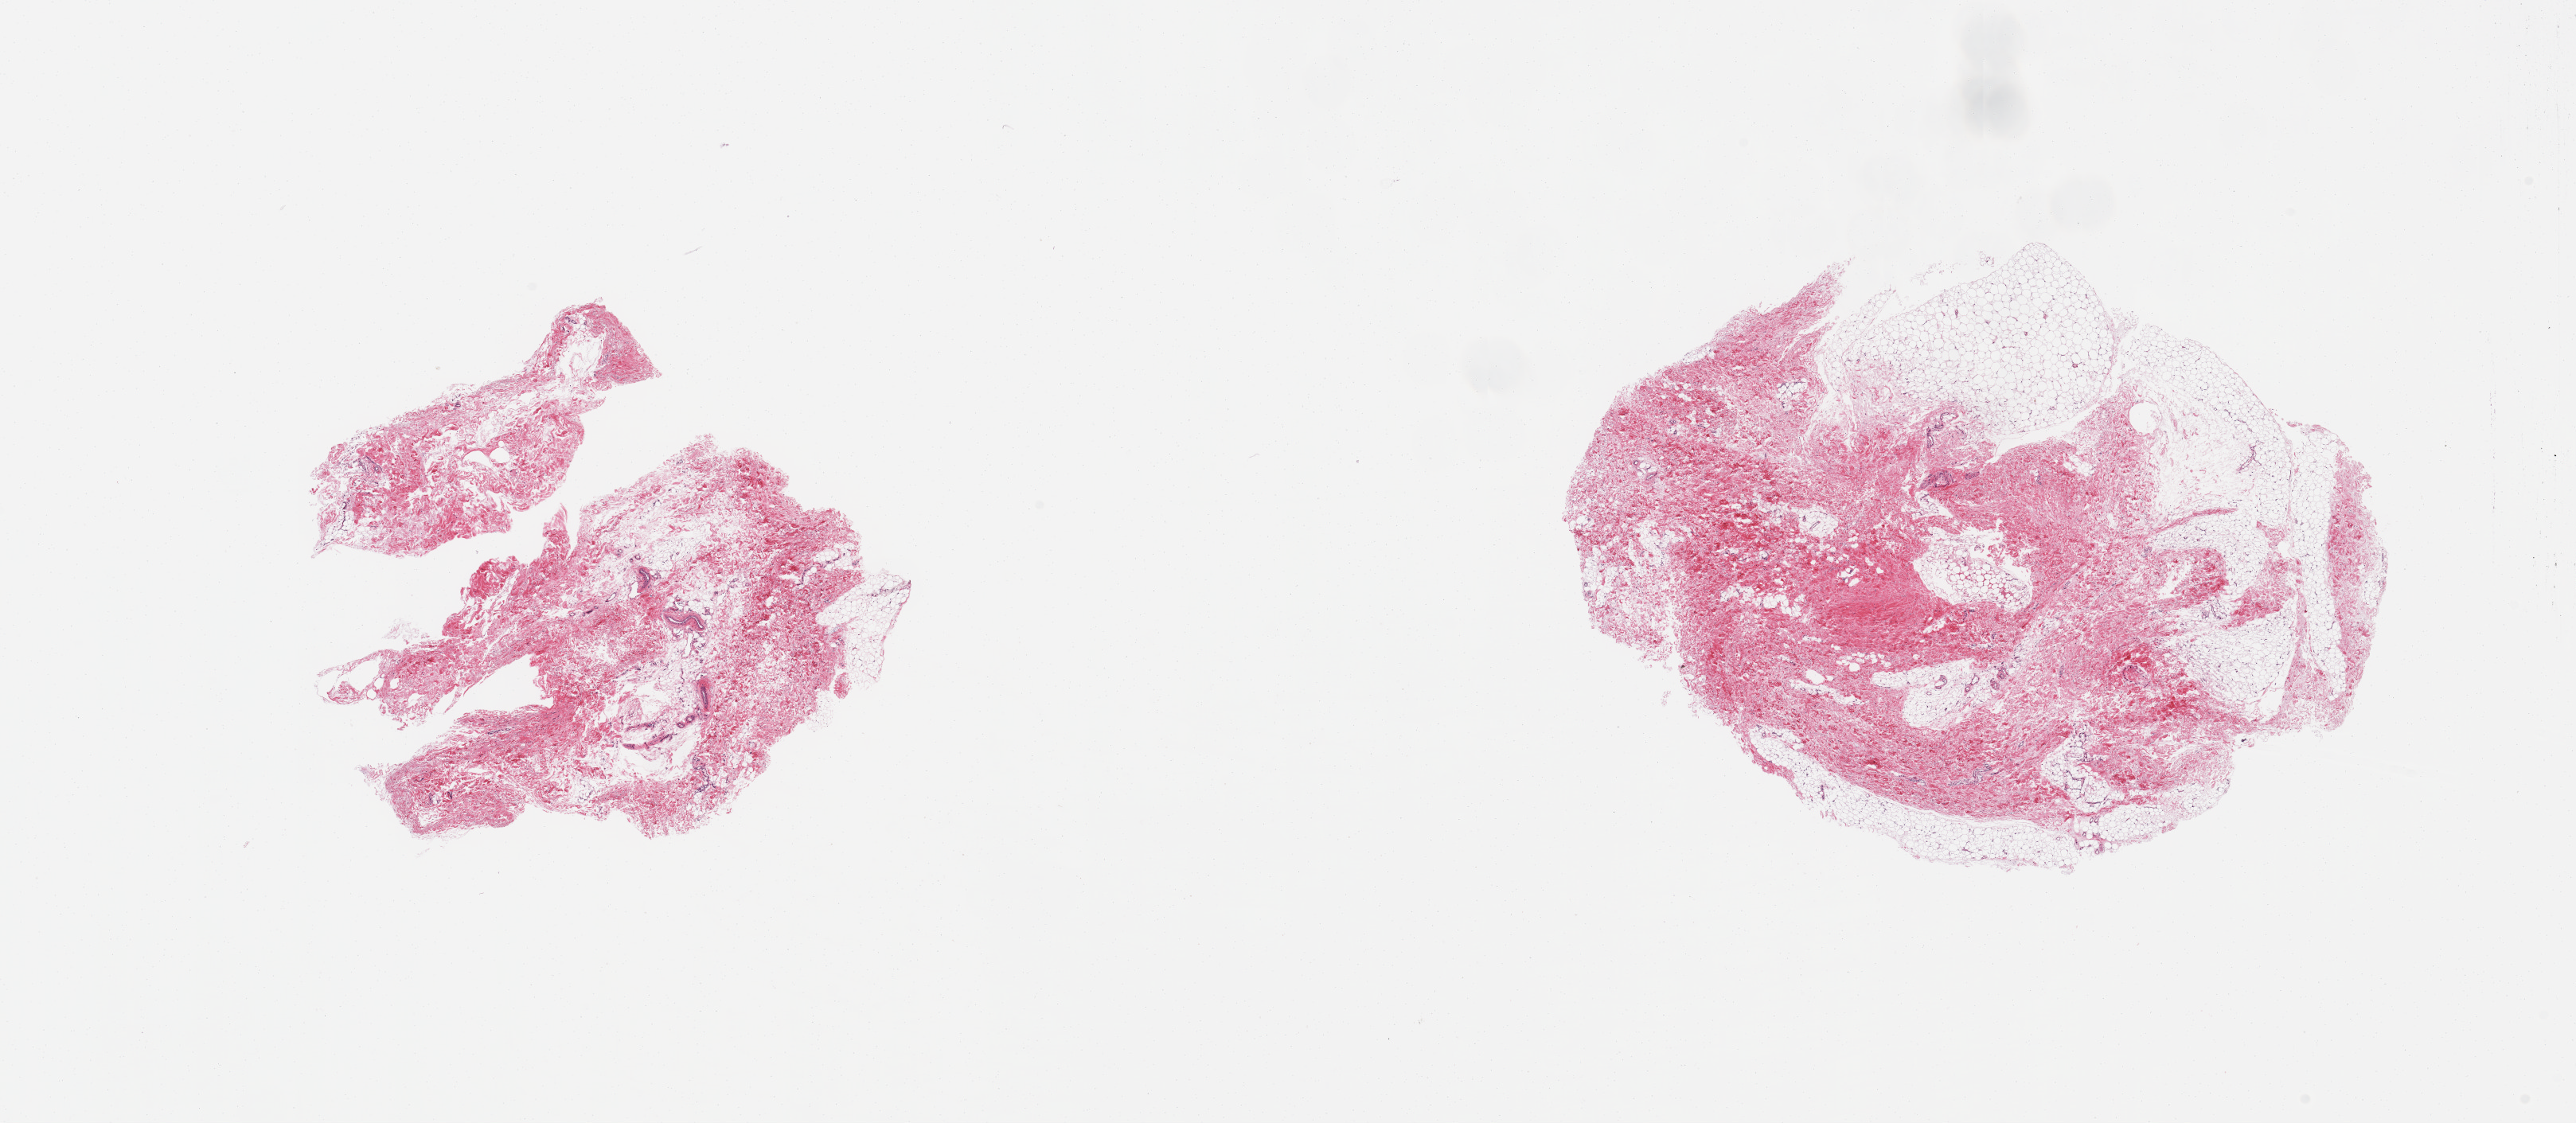
Whole-slide image, H&E stain, a low-resolution overview of the entire scanned area, about 25.6 x 11.2 mm (from a 20x scan), PAXgene-fixed, paraffin-embedded tissue, section of breast (target tissue), tissue donor sample. Donor sex: male.
Reviewer comment on this tissue sample: 2 pieces, fibroadipose elements only.